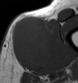
MRI of an extremity soft-tissue mass, one axial slice. Position 16 of 43 along the scan axis. MR volume resampled by the dataset authors to the PET/CT grid (not the native acquisition matrix). 78 × 83 image matrix, field of view 76 × 81 mm. Male patient. From the clinical record (not read from this slice): histological type: pleiomorphic leiomyosarcoma; grade: high; site of the primary tumour: left thigh.
Outlined on this slice (expert contour drawn on MRI and transferred to this co-registered scan by the dataset authors):
- gross tumour volume including surrounding oedema: box from (x=9, y=15) to (x=60, y=68) px
- gross tumour volume (mass): (x=9, y=17)–(x=55, y=68)